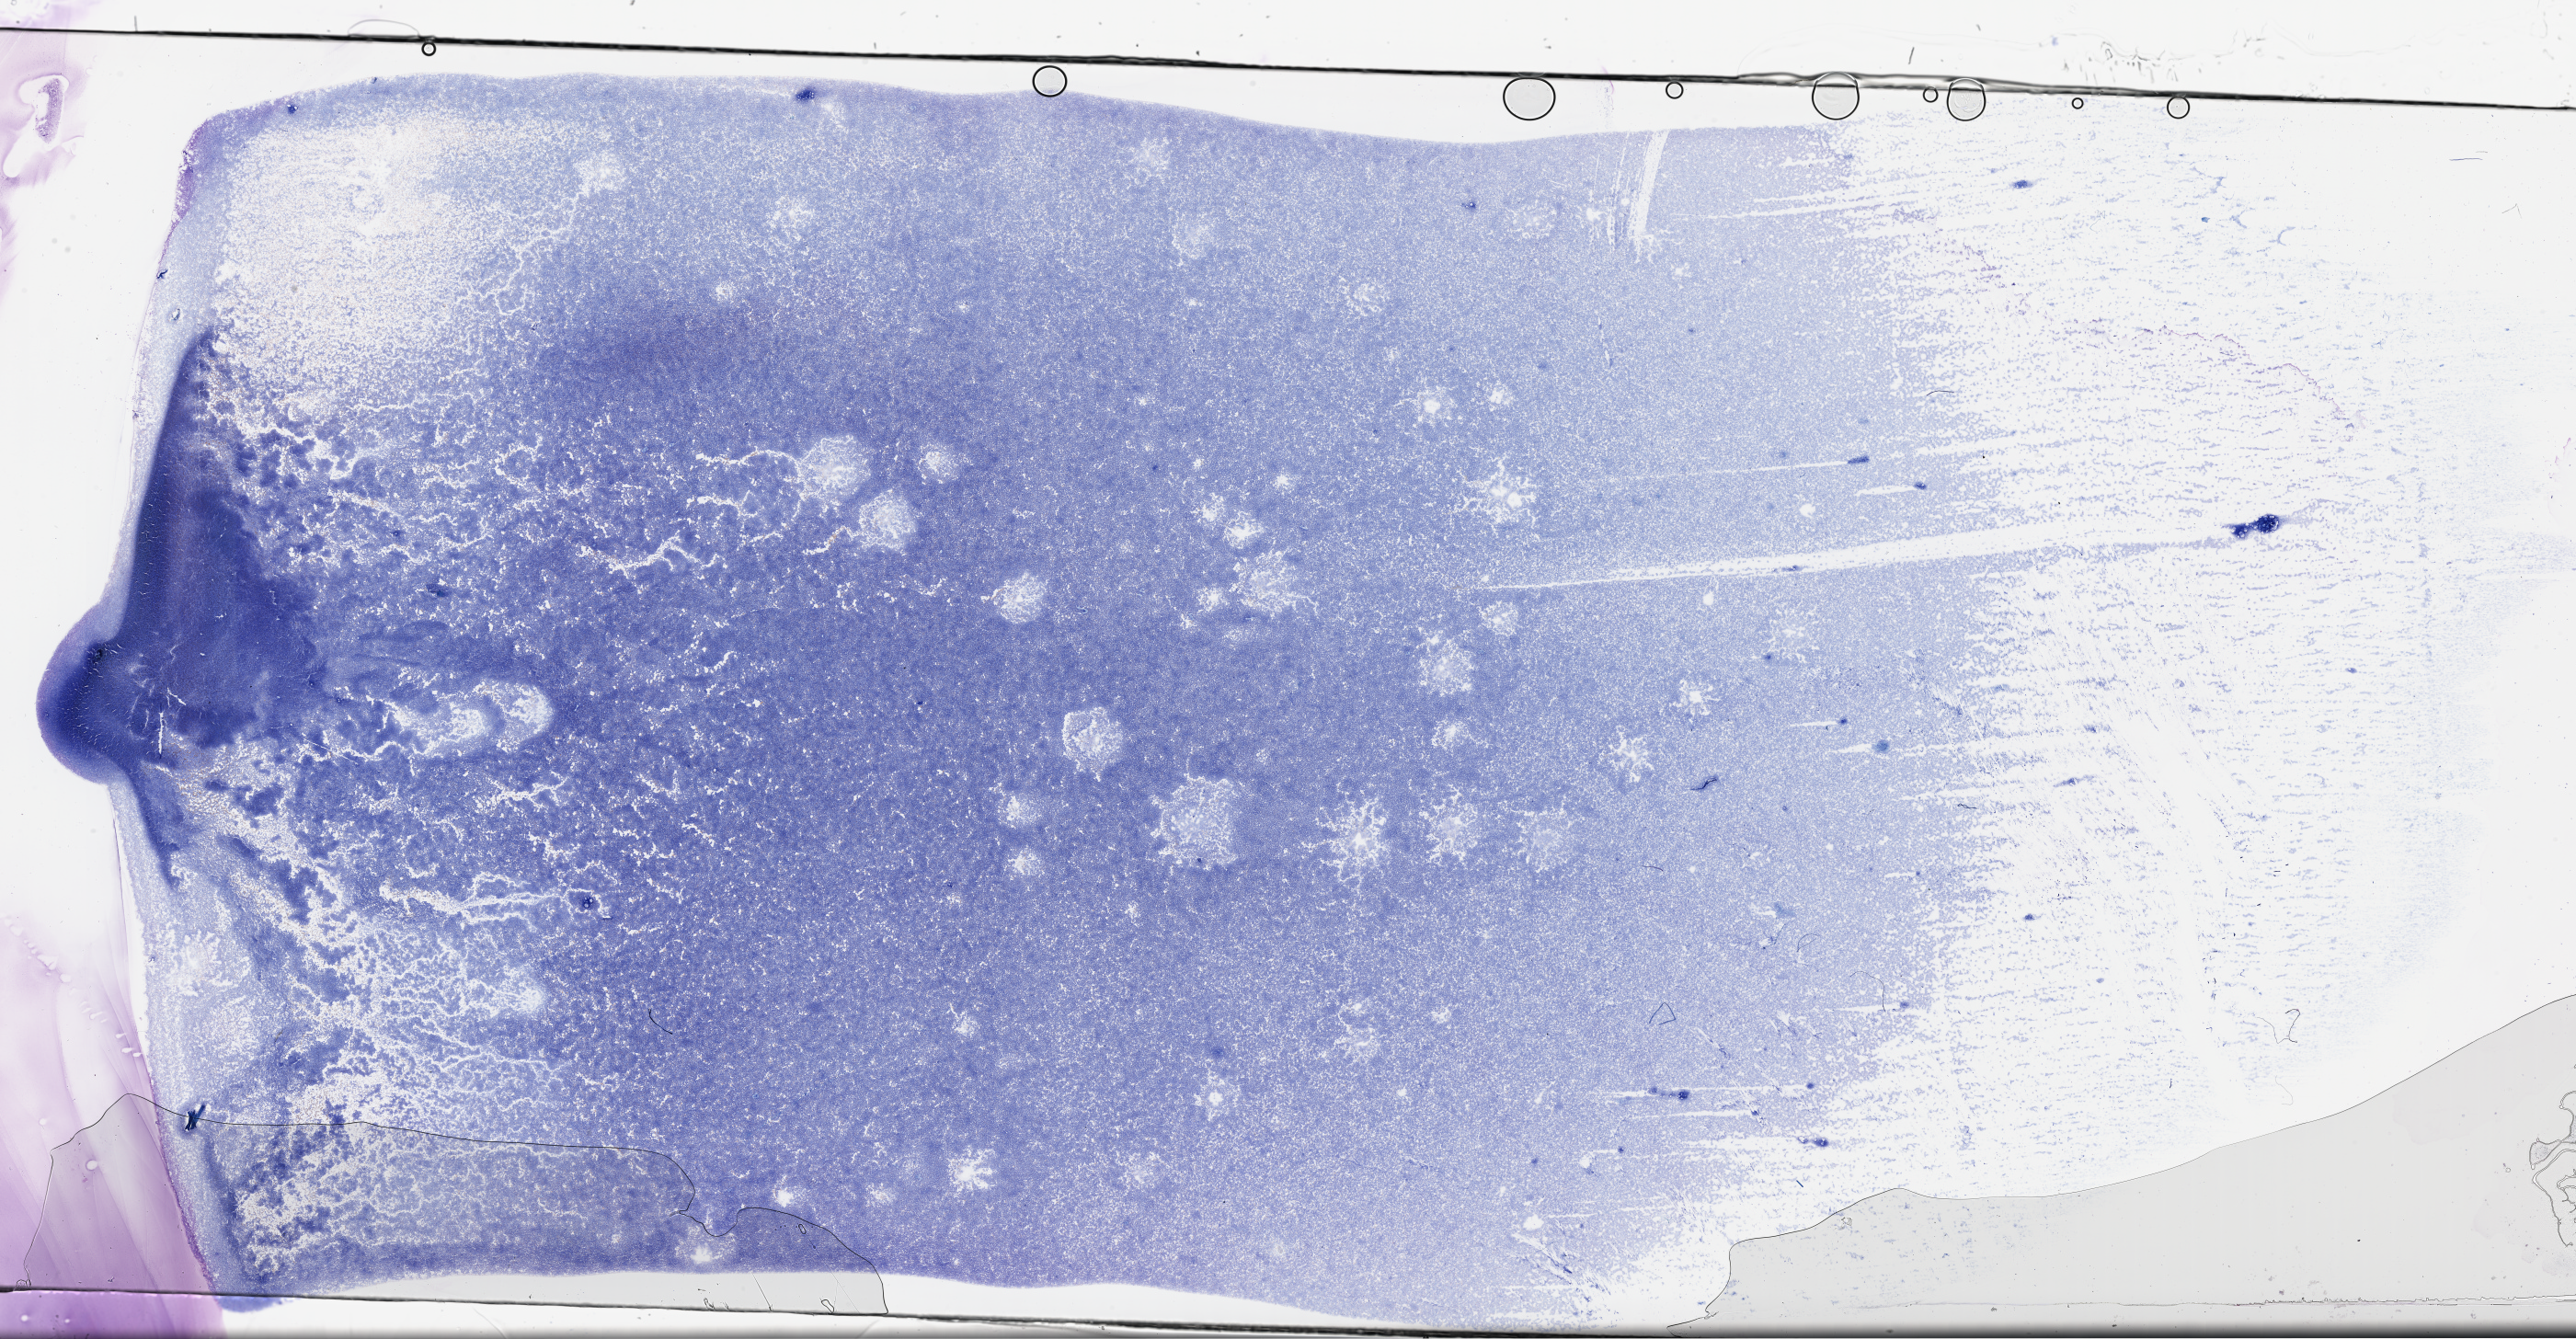
Whole-slide histology image, H&E-stained — shown as a low-resolution overview of the whole scanned area (about 45.2 x 23.5 mm, acquisition: 40x scan); bone marrow (leukaemic) sample. 70-year-old female patient. Blasts: 80%.
Diagnosis: Acute Myeloid Leukemia. FAB classification: M1.